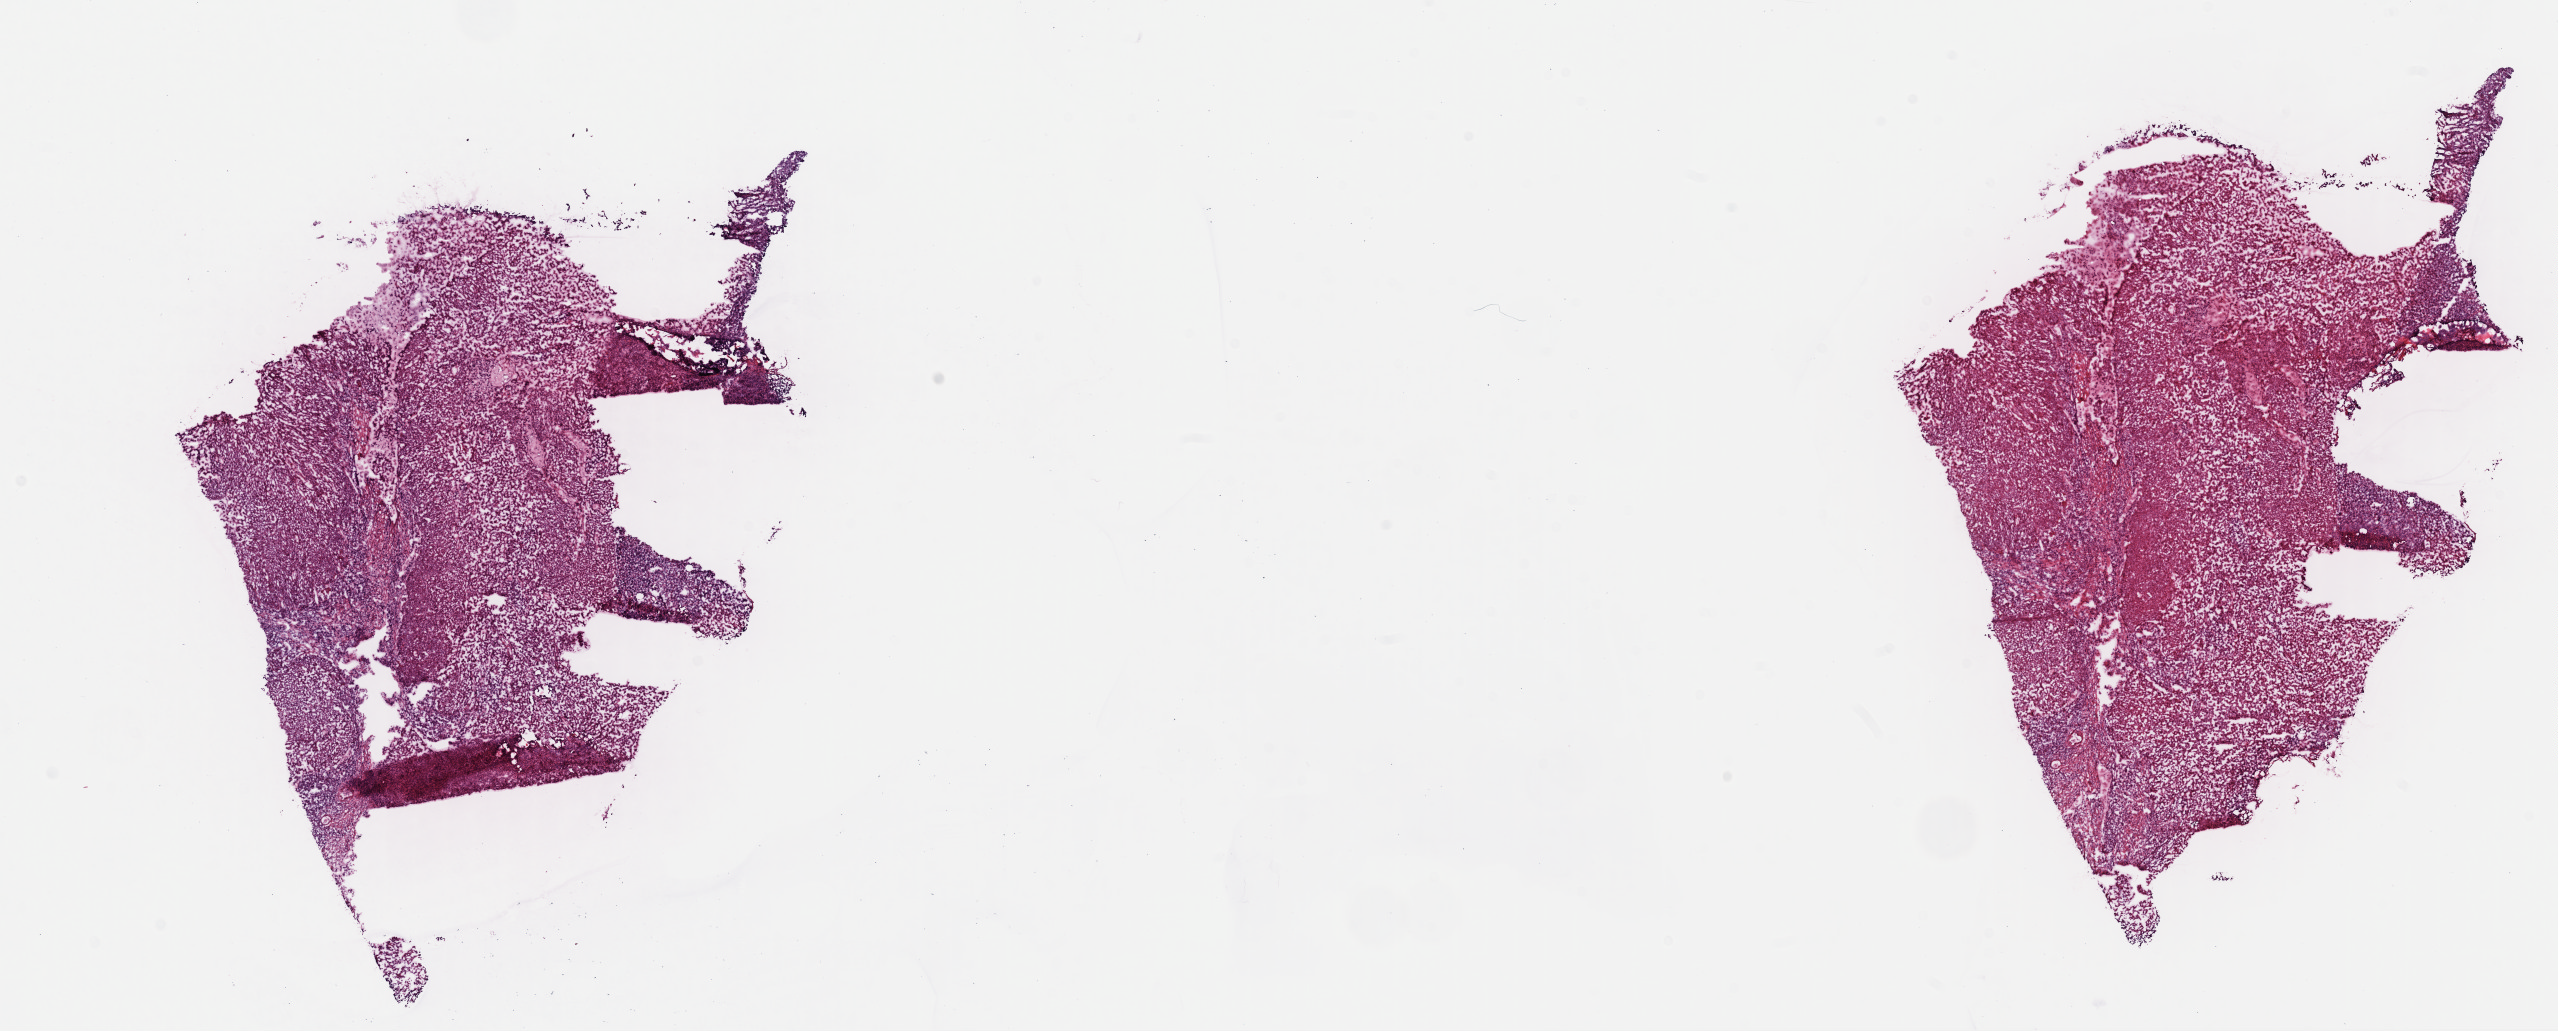
Hematoxylin and eosin (H&E) stained whole-slide image, a low-resolution overview of the entire scanned area, about 20.2 x 8.1 mm (acquisition: 40x scan), frozen section from the top of the tissue portion, primary tumour sample from the cervix. Female, age 47 years at initial diagnosis. Histologic grade: G2 (moderately differentiated). Composition of this section per pathologist review: tumour cells 85%, tumour nuclei 85%, normal cells 0%, stromal cells 13%, necrosis 2%. Inflammatory infiltration, as recorded: lymphocyte infiltration 10%, monocyte infiltration 0%, neutrophil infiltration 0%.
FIGO stage: IB1. Histologic diagnosis: Squamous cell carcinoma, large cell, nonkeratinizing, NOS (cervix uteri).